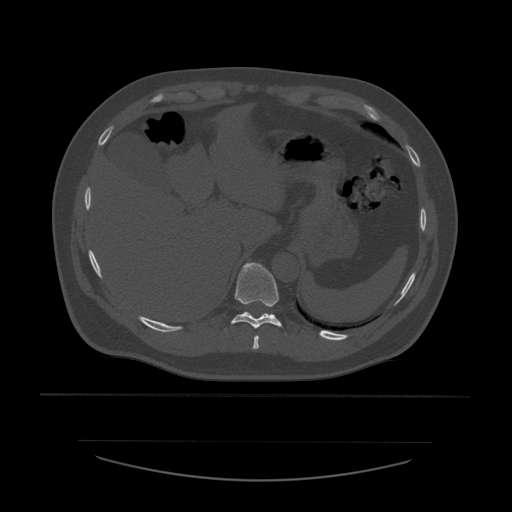
CT including the spine, one axial slice; slice 296 of 532 in the series (ordered by position); reconstruction kernel STANDARD; bone window (W 1800 / L 400 HU); 1.25 mm slice thickness; 512 × 512 image matrix, field of view 441 × 441 mm. Patient age 44 years. Case-level facts recorded for this patient, not image findings: primary cancer: soft tissue sarcoma.
Annotated regions visible in this slice (semi-automatic segmentation, software-assisted and operator-edited):
- T10 vertebra: box from (x=225, y=263) to (x=283, y=331) px
- T9 vertebra: (x=253, y=336)–(x=260, y=350)